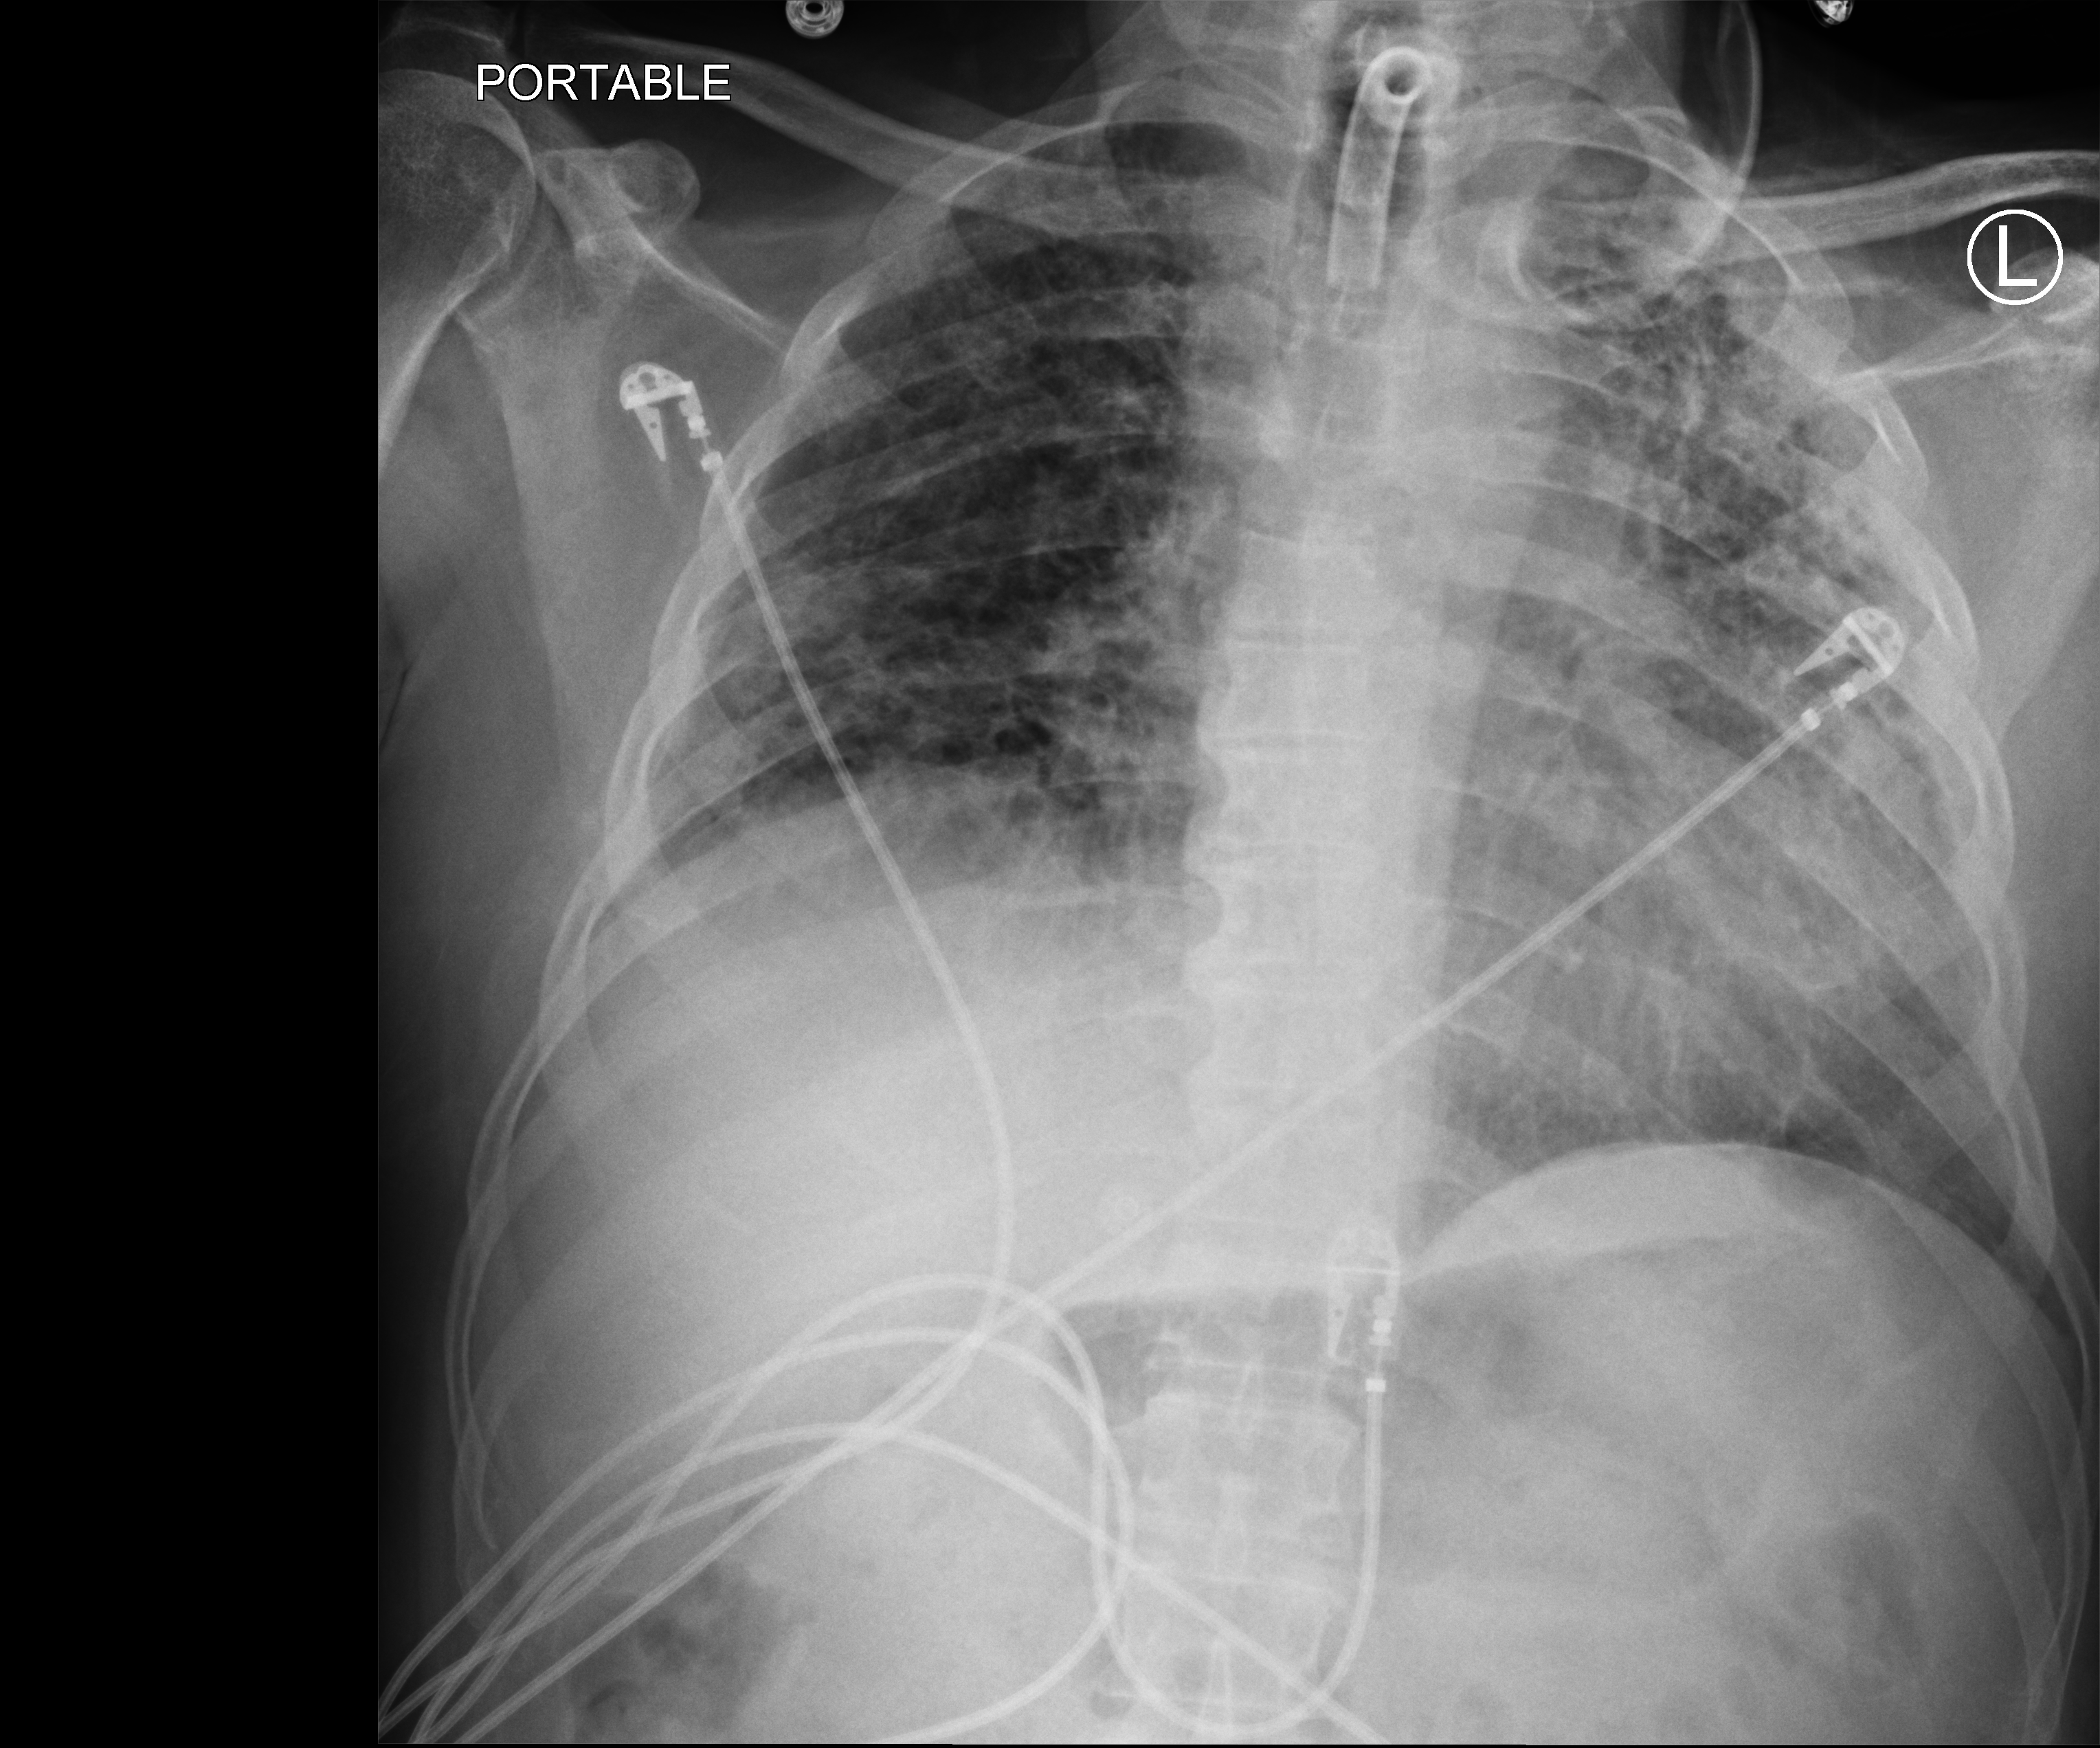
Chest X-ray (portable); anteroposterior (AP) projection. Patient hospitalised with COVID-19; male, aged 18–59 years.
From the hospital-stay record, not from the radiograph (when in the stay this image was taken is not recorded): admitted to intensive care during this hospital stay: yes.